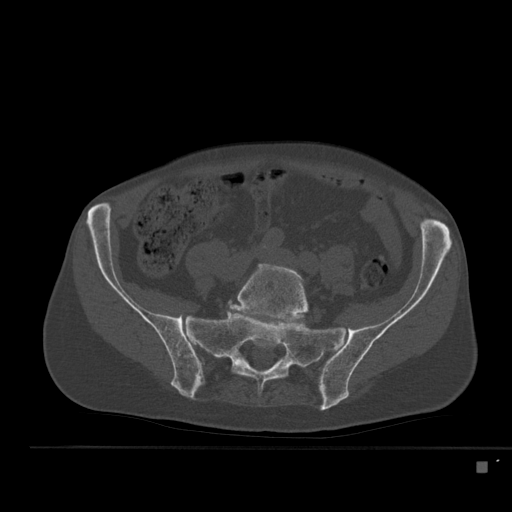
CT including the spine, one axial slice. Slice 114 of 517 in the series (ordered by position). Reconstruction kernel Br40s. 120 kVp. Bone window (W 1800 / L 400 HU). 1.5 mm slice thickness. 512 × 512 image matrix. Male patient, age 70 years. From the clinical record (not read from this slice): primary cancer: renal; vertebrae with lytic lesions (as recorded): T4, T6, T10, T12, L3, L4, L5.
Annotated regions visible in this slice (semi-automatically segmented with operator editing):
- L5 vertebra: bounding box [x1, y1, x2, y2] px = [229, 263, 312, 323]